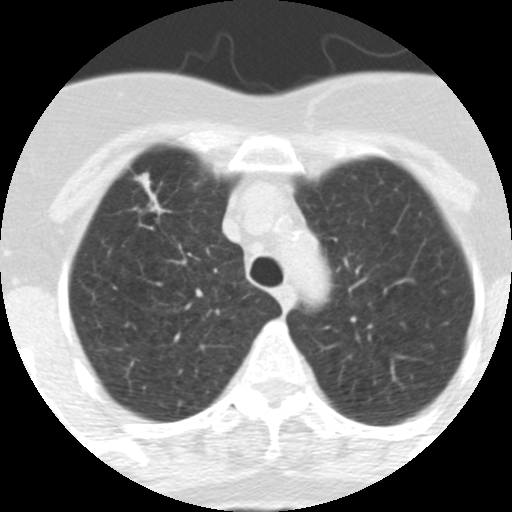
Low-dose screening chest CT, one axial slice; position 249 of 313 along the scan axis; reconstruction kernel STANDARD; 120 kVp; lung window (W 1500 / L -600 HU); 512 × 512 image matrix, field of view 253 × 253 mm.
Structures marked on this image (expert manual segmentation):
- lesion 1 (tumor, upper lobe of right lung): box from (x=134, y=173) to (x=164, y=214) px